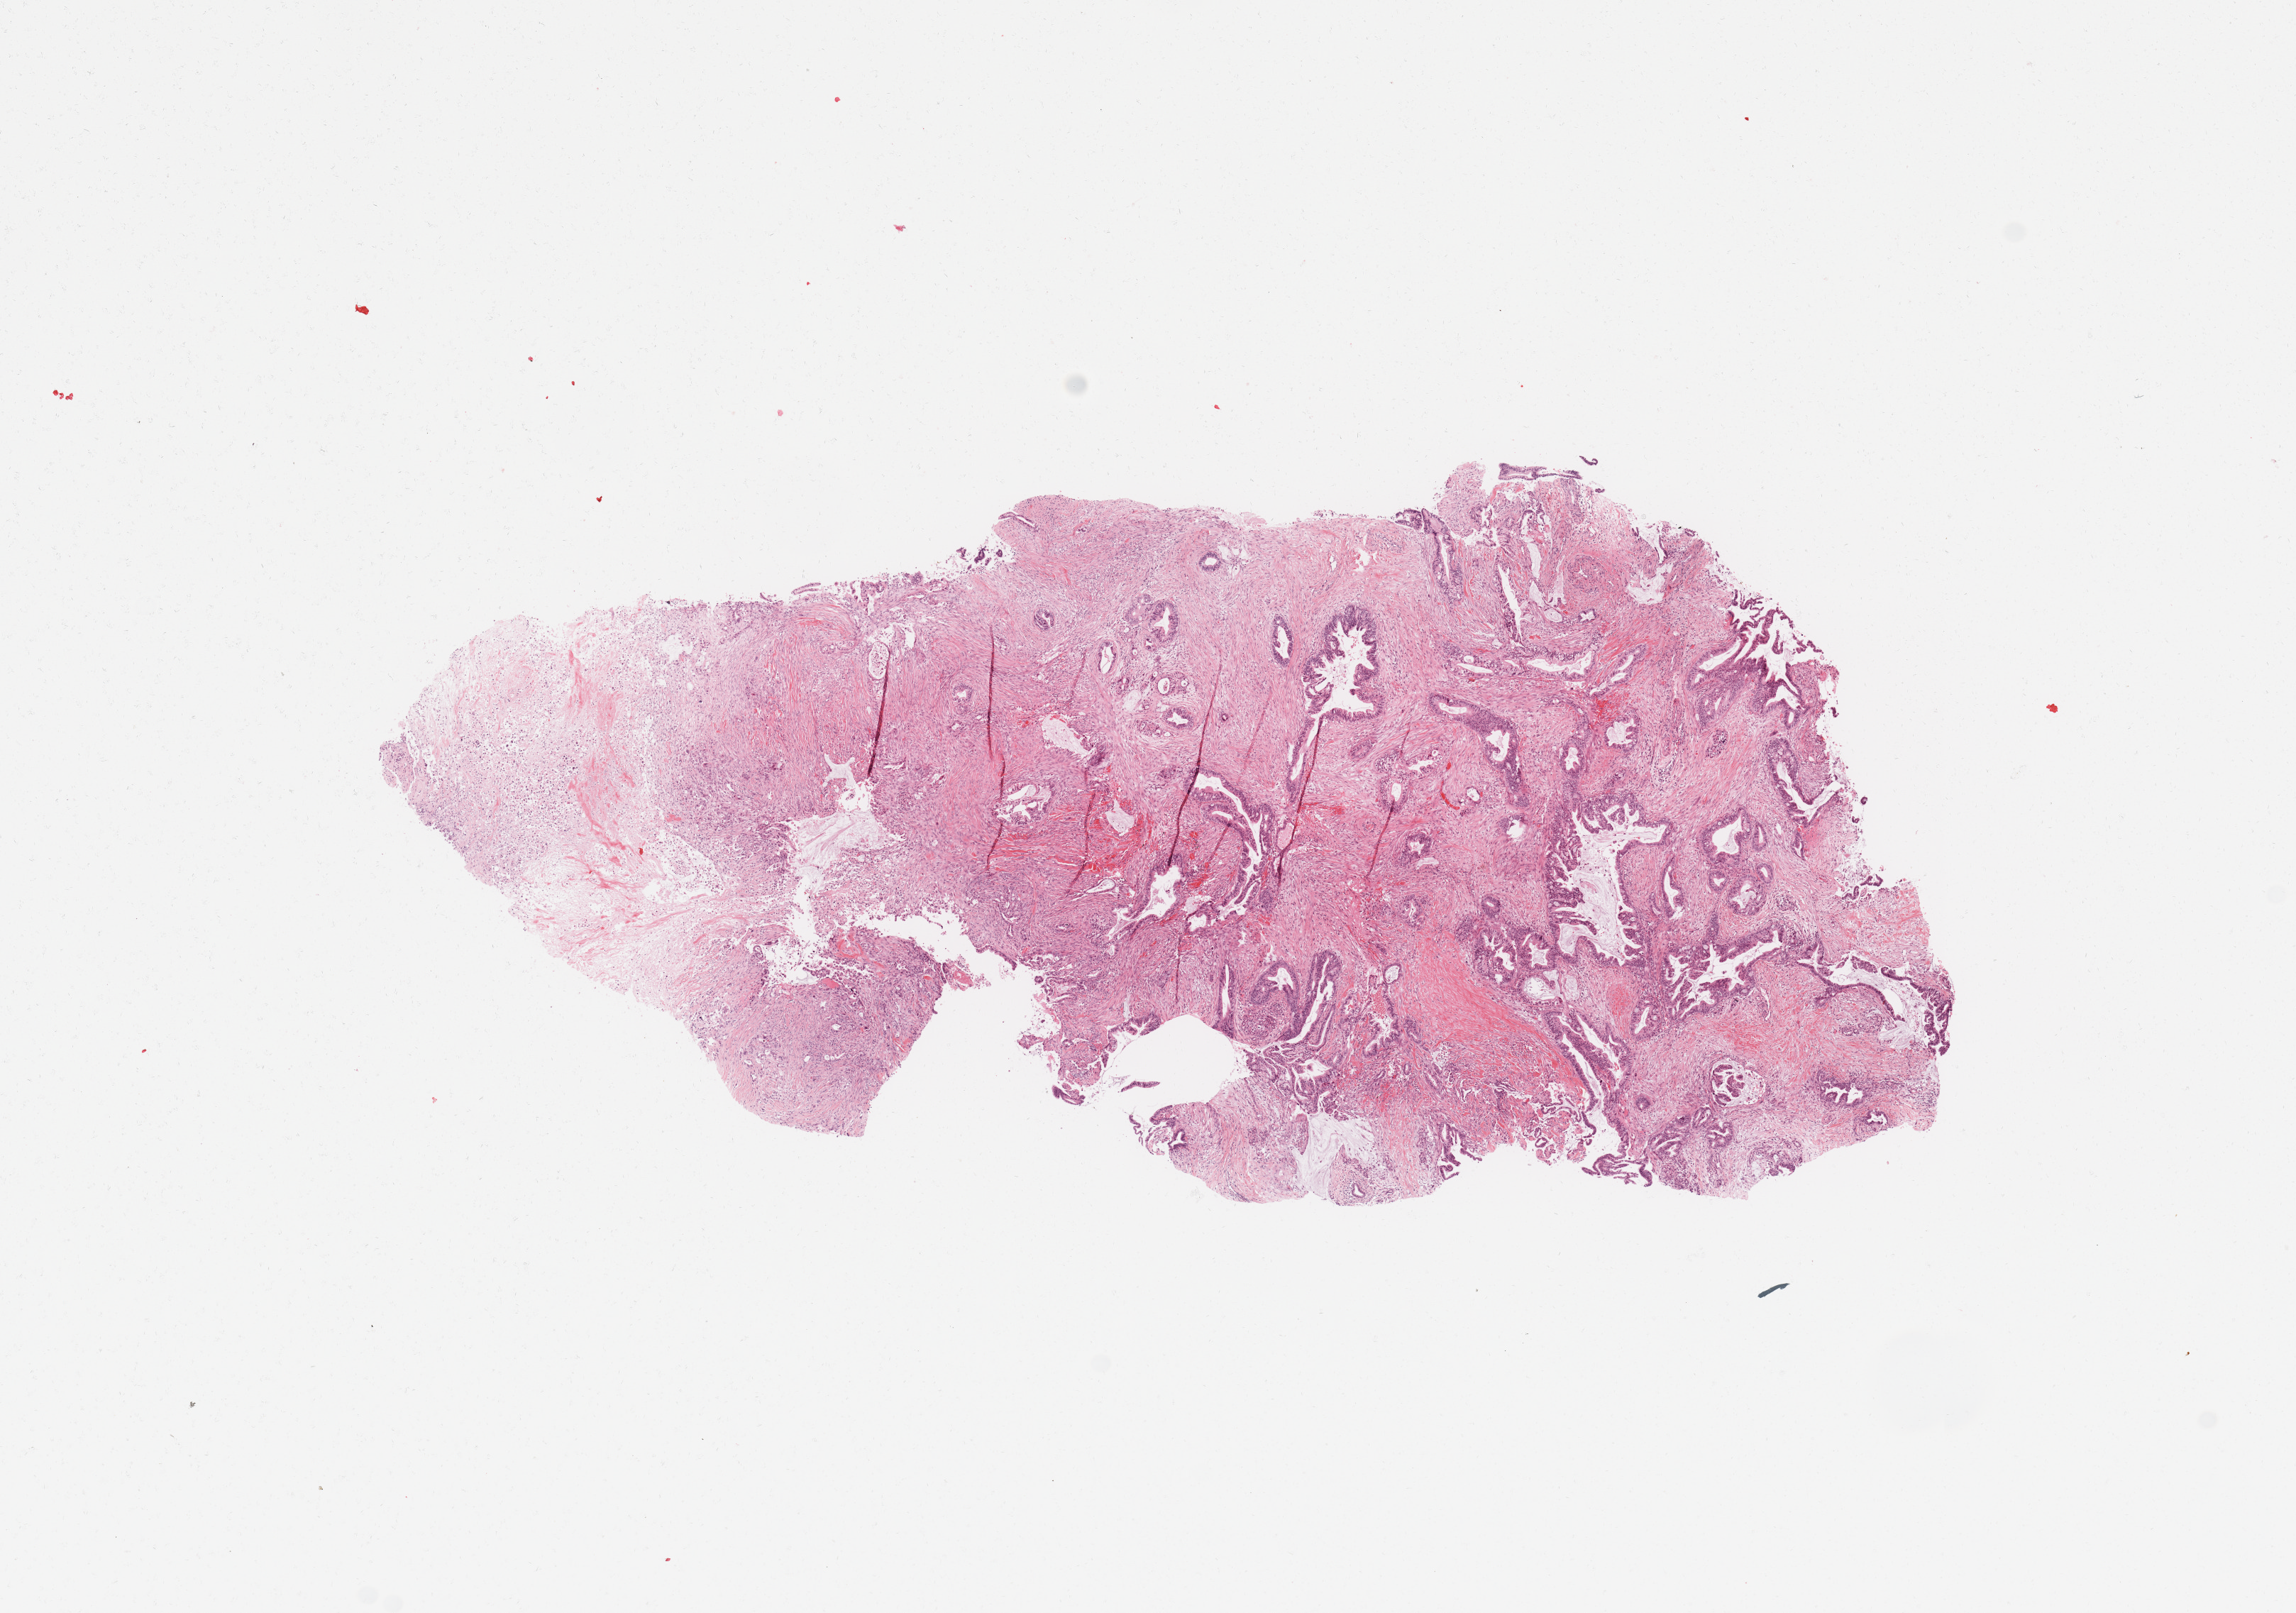
Digitized H&E tissue section (whole slide), whole scanned area (about 12.8 x 9.0 mm, slide scanned at 20x) shown as a low-resolution overview; tumour tissue sample, sampled site: pancreas. Female, 51 y/o. Histologic grade: G2 (moderately differentiated). Pathologist review of this section (percent, as recorded): tumour nuclei 30%, necrosis 0%.
* AJCC pathologic stage: IA
* histologic diagnosis: Infiltrating duct carcinoma, NOS
* primary tumour site (as recorded): head